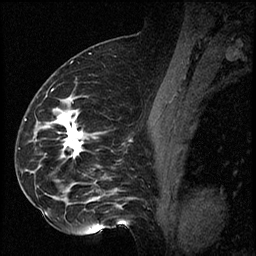
Breast MRI (dynamic contrast-enhanced), one sagittal slice; position 40 of 60 along the scan axis; dynamic contrast-enhanced series, image 2 of 2 at this slice position (ordered by acquisition); 1.5 T; TE 4.2 ms, TR 17.3 ms; 256 × 256 image matrix. Female patient. From the clinical record (not read from this slice): setting: breast cancer imaged before/during neoadjuvant chemotherapy; receptor status: HR-positive, HER2-negative.
Outlined on this slice (semi-automatic segmentation, software-assisted and operator-edited):
- analysis volume of interest (the breast-tissue region the enhancement analysis was run in; not a lesion): bounding box <41,93,115,223> (left, top, right, bottom; pixels)
- tumour enhancement mask (voxels above the 100 % enhancement threshold inside the analysis volume of interest): <58,112,82,157>